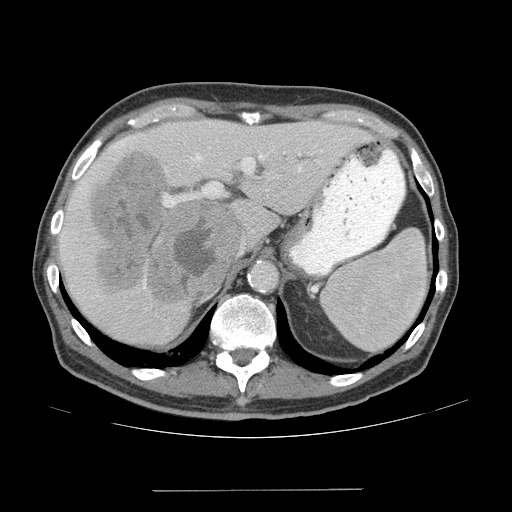
Contrast-enhanced abdominal CT (liver protocol), one axial slice; slice 45 of 77 in the series (ordered by position); 140 kVp; soft-tissue window (W 400 / L 40 HU); 512 × 512 image matrix. From the clinical record (not read from this slice): diagnosis: hepatocellular carcinoma (patient treated with transarterial chemoembolisation; whether this scan precedes or follows treatment is not stated here); TNM stage (as recorded): Stage-IVA; Child-Pugh class: A; tumour differentiation: well differentiated.
Outlined on this slice (semi-automatic segmentation, software-assisted and operator-edited):
- liver parenchyma outside the tumour (the mass and vessels are separate outlines, so this box may not span the whole liver): box from (x=58, y=120) to (x=372, y=344) px
- mass: (x=91, y=149)–(x=241, y=303)
- liver vessels: (x=61, y=137)–(x=322, y=297)